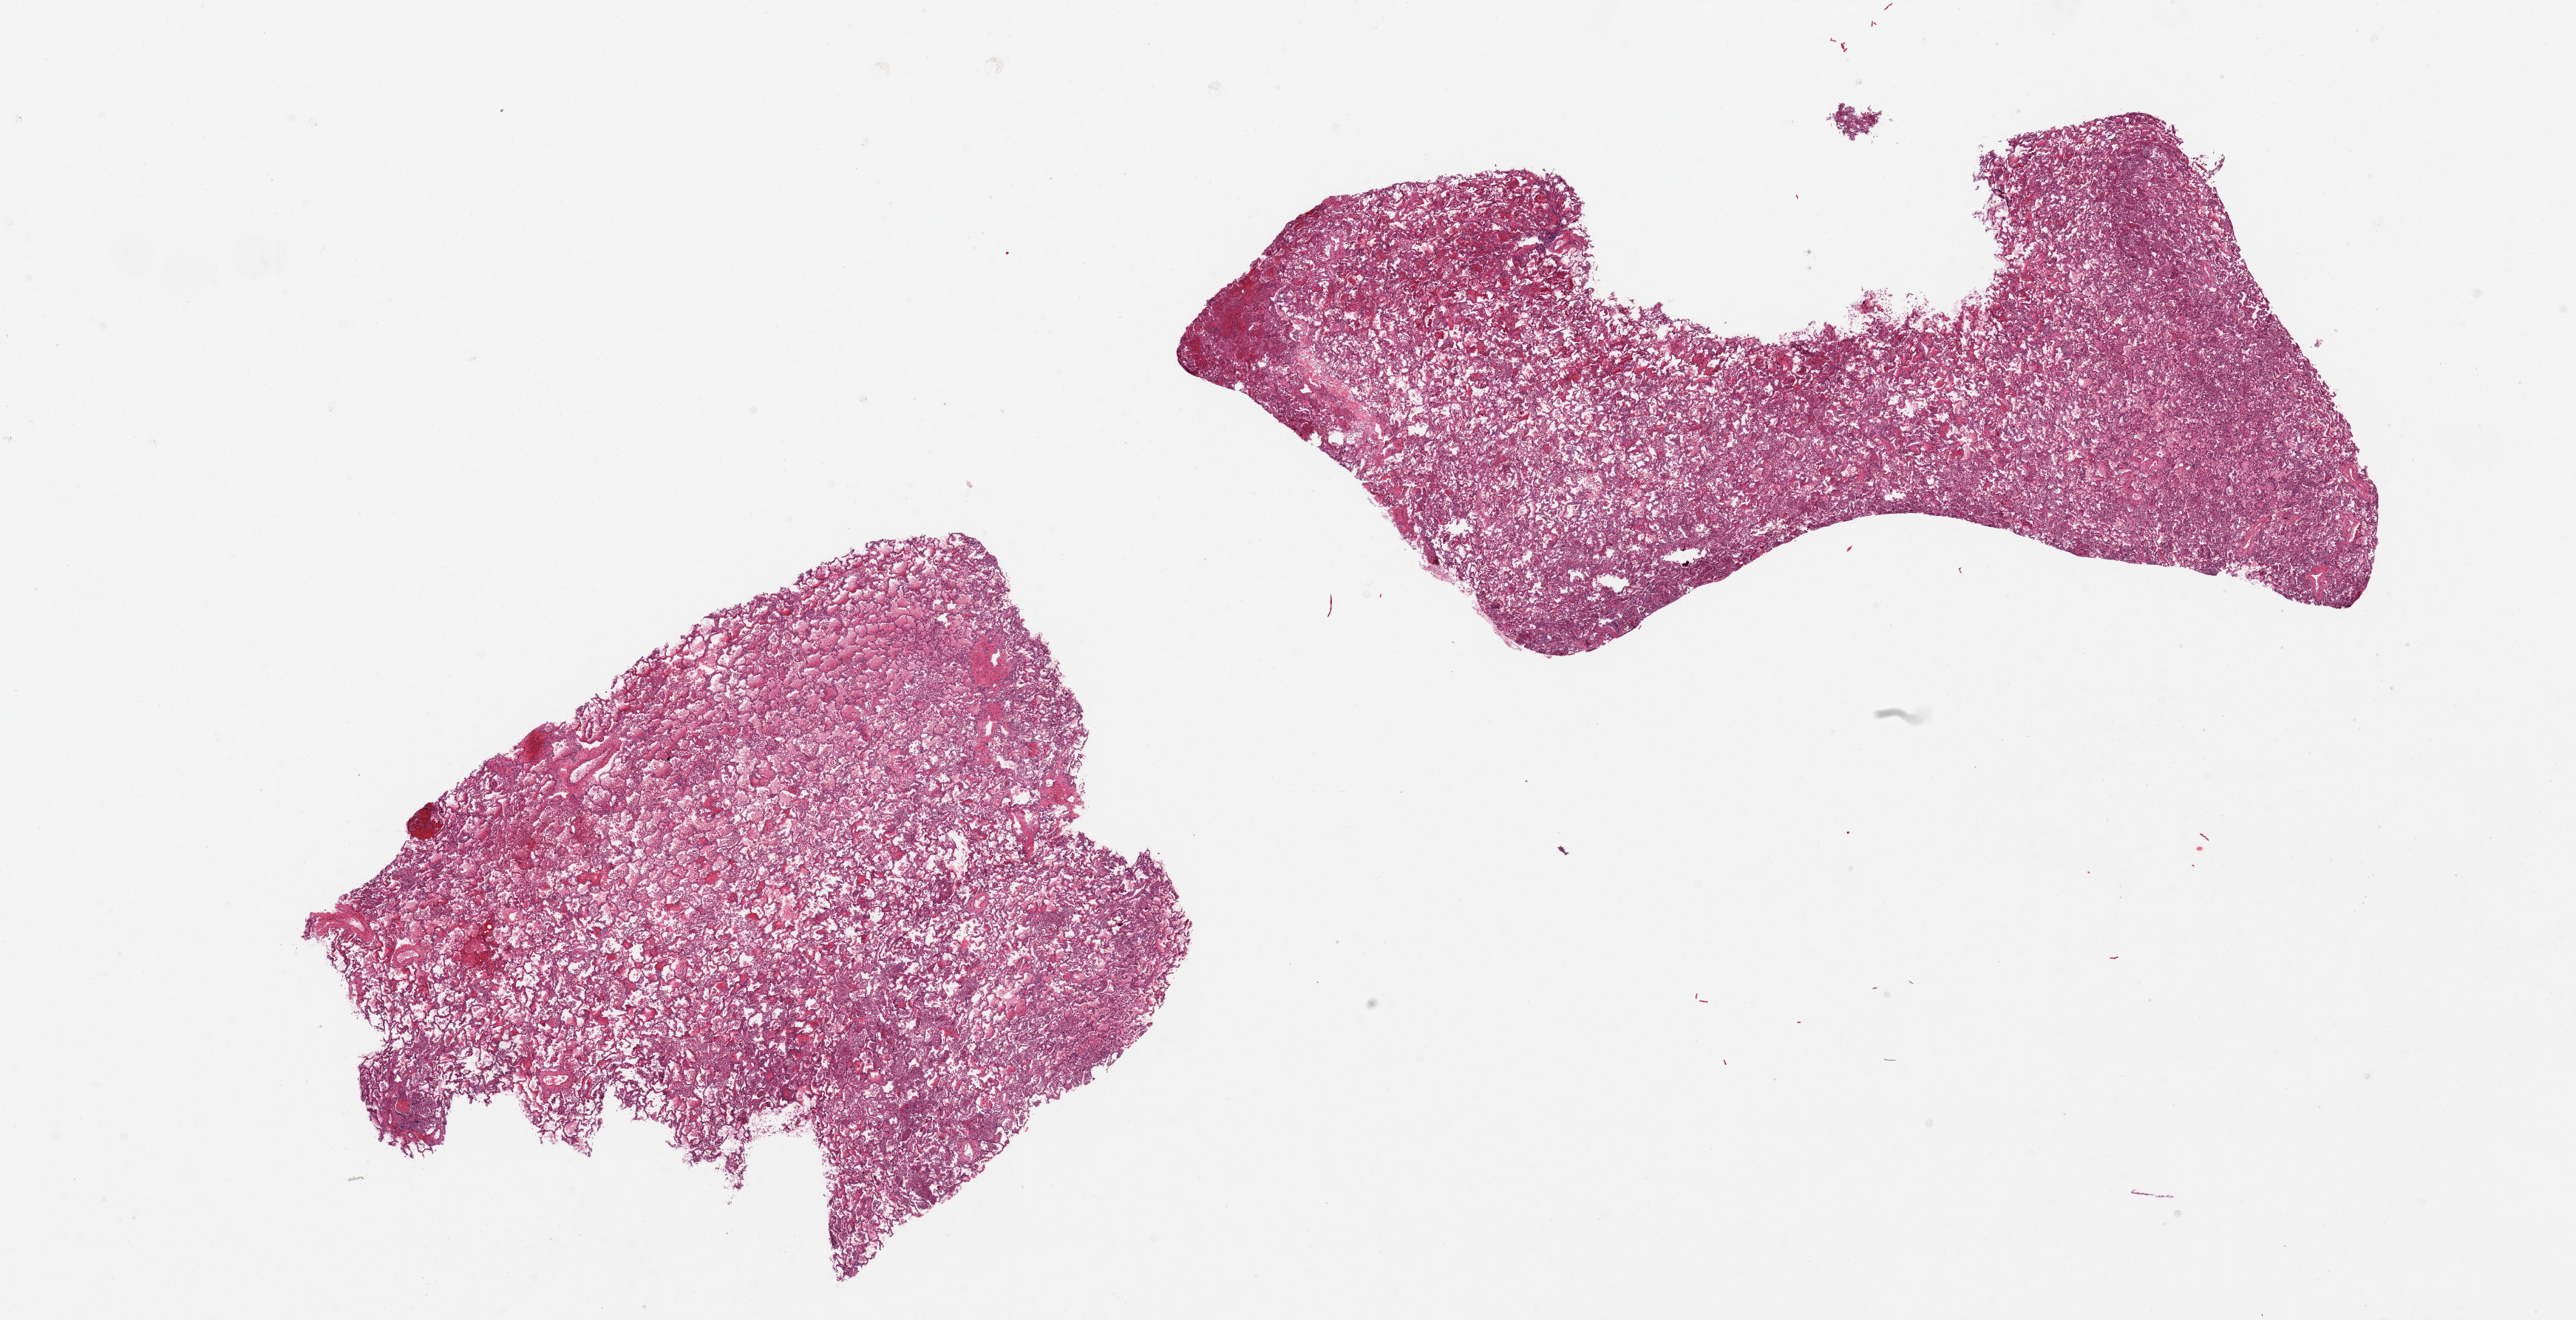
H&E whole-slide image, brightfield, a low-resolution overview of the entire scanned area, about 27.6 x 14.1 mm, PAXgene-fixed, paraffin-embedded tissue, target tissue: lung, donor tissue sample. Donor sex: male.
- pathologist's review note for this sample: 2 aliquots, ~9x7mm. Diffuse mild chronic active pneumonitis and edema